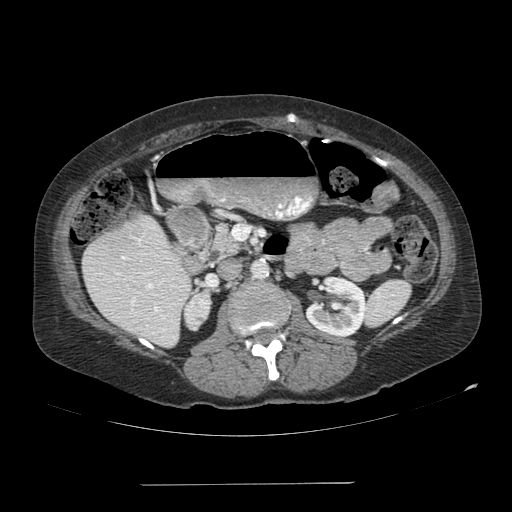
Contrast-enhanced abdominal CT, one axial slice; slice 48 of 113 in the series (ordered by position); 120 kVp; soft-tissue window (W 400 / L 40 HU); 2.5 mm slice thickness; 512 × 512 image matrix. Female patient, age 67 years. Case-level facts recorded for this patient, not image findings: diagnosis: adrenocortical carcinoma; tumour side: right adrenal; tumour size at pathology: 9.8 cm; Ki-67 index: 59 %; stage (as recorded): 4.
Outlined on this slice (semi-automatic segmentation, software-assisted and operator-edited):
- mass: bounding box (x1, y1, x2, y2) in pixels: (185, 293, 209, 329)